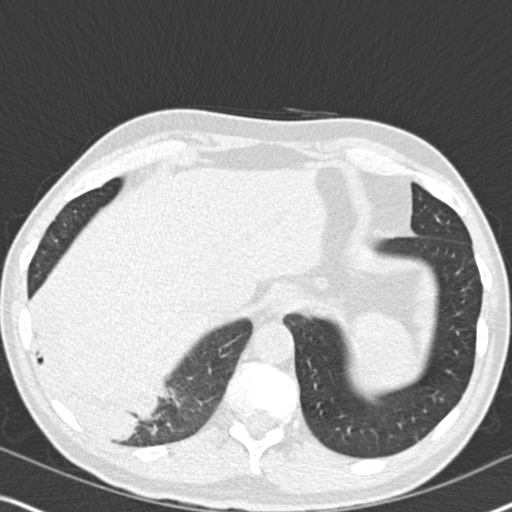
Low-dose screening chest CT, axial slice, second screening round (one year after baseline), lung window (W 1500 / L -600 HU), 2 mm slice thickness, 512 × 512 image matrix. Male, age 61 years at enrolment. Current smoker at enrolment.
• Lesion marked by an expert reader, box from (x=15, y=274) to (x=179, y=454) px.
• Reader record for this screening exam (exam-level; its link to the box is not recorded): non-calcified nodule or mass ≥4 mm, right lower lobe, 90 × 80 mm, soft tissue attenuation, pre-existing on the prior screen: yes; interval growth: yes.
• Later outcome: lung cancer diagnosed 20 days after this screen — bronchiolo-alveolar adenocarcinoma, NOS, right lower lobe, moderately differentiated (G2), stage IIIB (AJCC 6th edition), 90 mm at pathology.